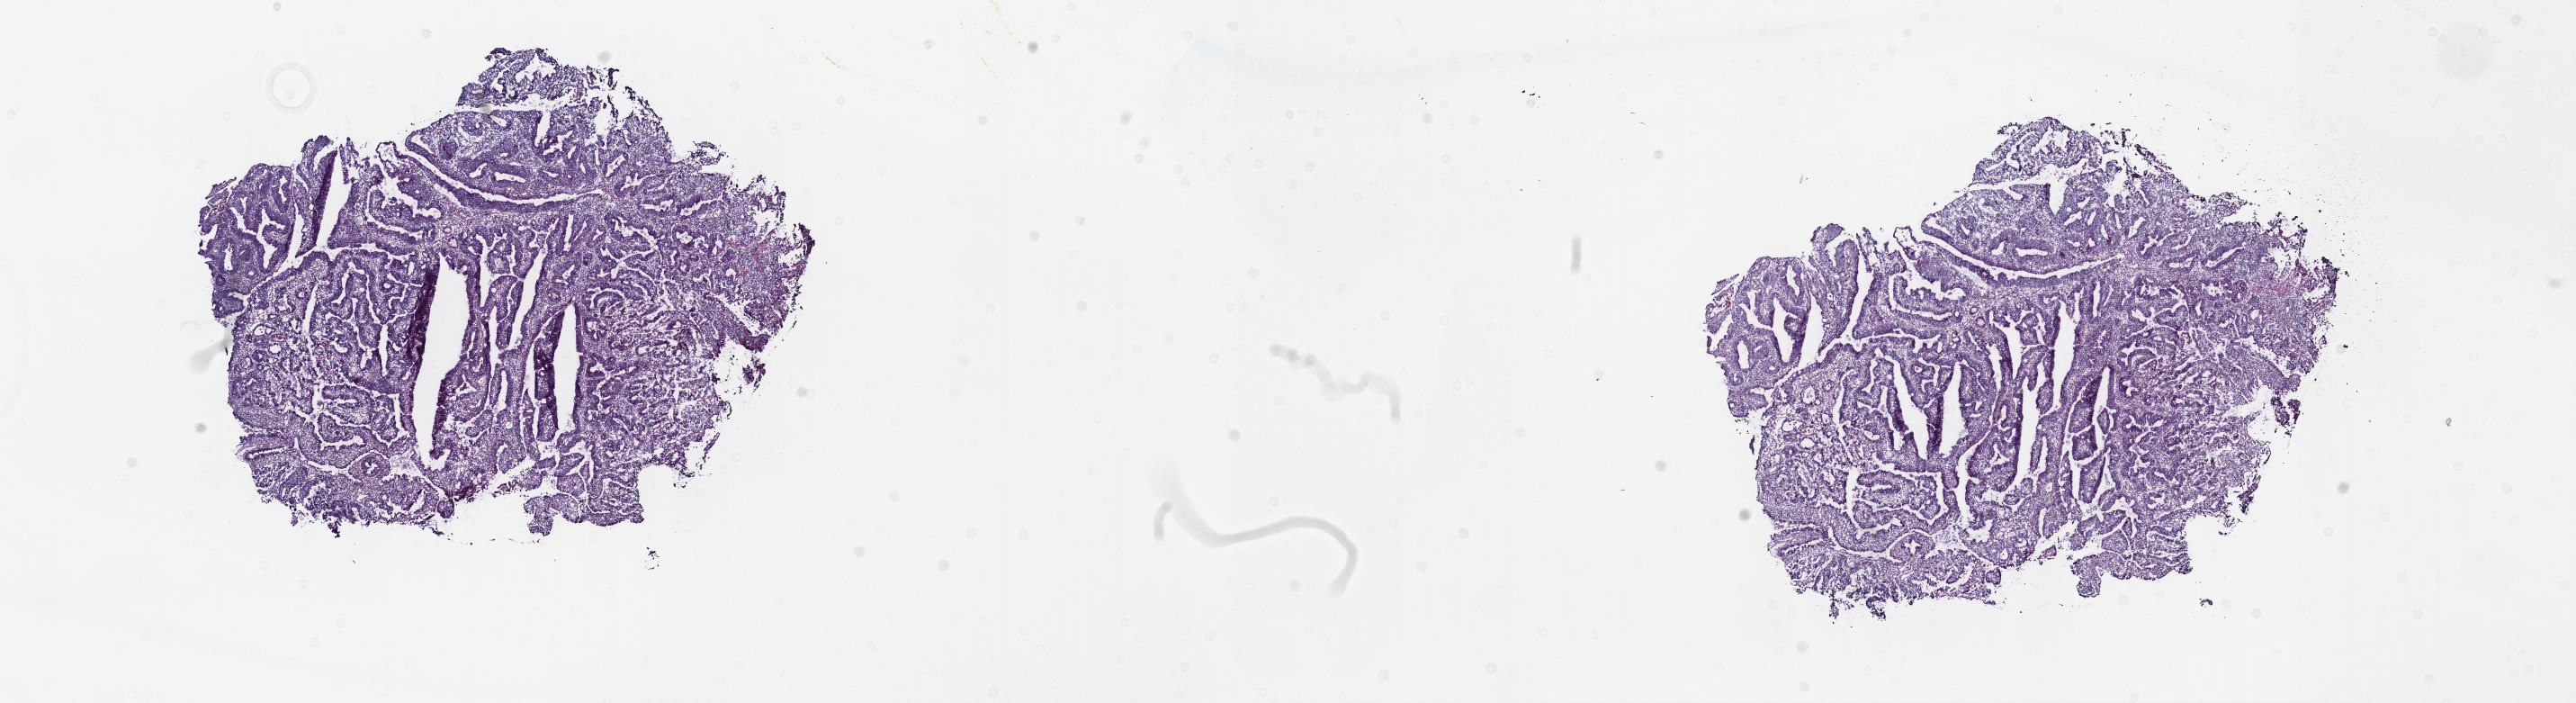
Whole-slide histology image, H&E — whole scanned area (about 23.2 x 6.3 mm) shown as a low-resolution overview, frozen section from the top of the tissue portion, primary tumour sample from the colon. Female patient; age at initial diagnosis 84 years. Composition of this section per pathologist review: tumour cells 80%, tumour nuclei 80%, normal cells 10%, stromal cells 5%, necrosis 5%. Inflammatory infiltration, as recorded: lymphocyte infiltration 8%, monocyte infiltration 0%, neutrophil infiltration 2%.
* AJCC pathologic stage: I
* diagnosis: Adenocarcinoma, NOS (ascending colon)